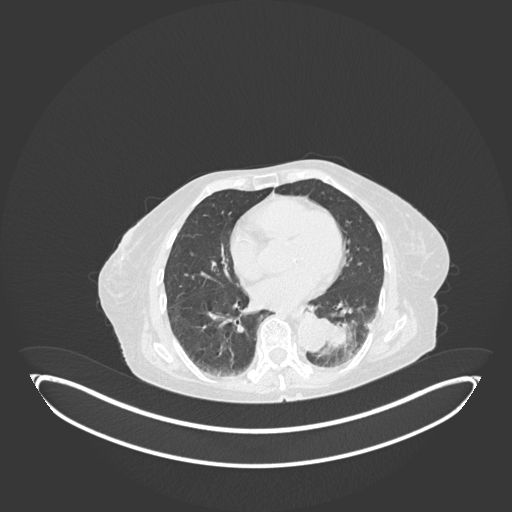
Chest CT, one axial slice; position 43 of 189 along the scan axis; lung window (W 1500 / L -600 HU); 1 mm slice thickness; 512 × 512 image matrix. Female patient, age 82 years. From the clinical record (not read from this slice): clinical TNM (as recorded): T1b N0 M1.
Structures marked on this image (bounding box drawn by a radiologist):
- lung tumour (recorded histology: adenocarcinoma): bounding box (x1, y1, x2, y2) in pixels: (315, 316, 353, 355)